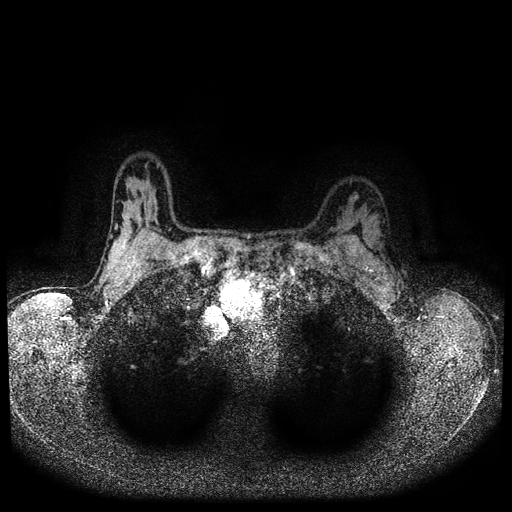
Breast MRI (dynamic contrast-enhanced, multi-phase), one axial slice; slice 79 of 116 in the series (ordered by position); dynamic contrast-enhanced series, time point 2 of 5 at this slice position (early post-contrast); 1.5 T; TE 2.7 ms, TR 5.4 ms; 2 mm slice thickness; 512 × 512 image matrix, field of view 330 × 330 mm. Female patient, age 32 years.
Structures marked on this image (semi-automatically segmented with operator editing):
- breast lesion (labelled benign in the annotation): bounding box (x1, y1, x2, y2) in pixels: (349, 191, 359, 203)